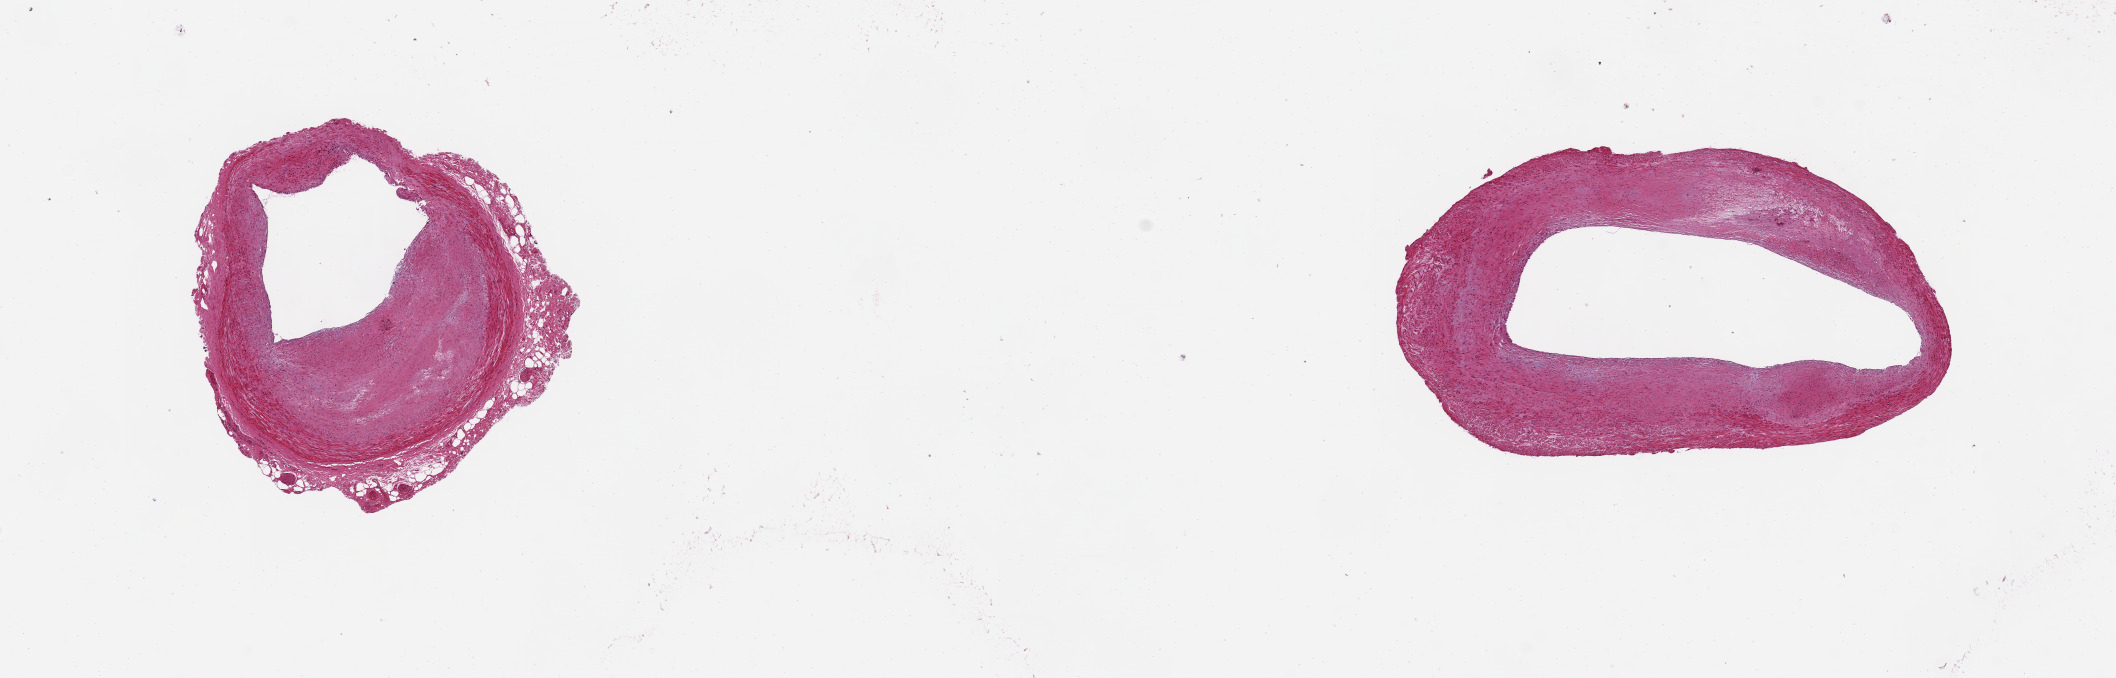
Hematoxylin and eosin (H&E) whole-slide image, brightfield — whole scanned area (about 16.7 x 5.4 mm) shown as a low-resolution overview; PAXgene-fixed, paraffin-embedded tissue; target tissue: coronary artery; donor tissue sample. Male donor.
* review note (as recorded): 2 pieces. 3x3 & 4x2.5mm; well trimmed; 1 with large, 1mm, eccentric plaque; 1 with 0.3 mm adventitial adipose